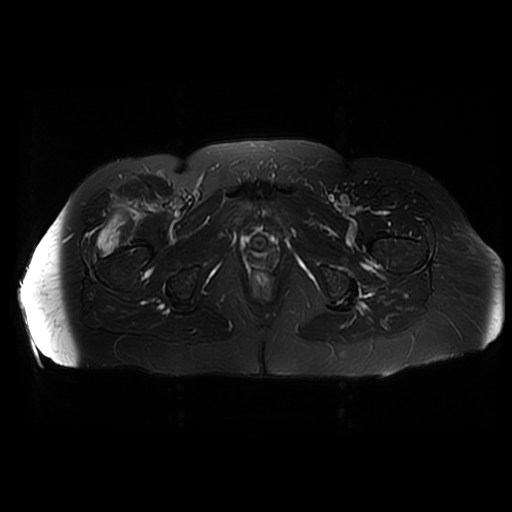
MRI of an extremity soft-tissue mass, one axial slice. Position 34 of 42 along the scan axis. T2-weighted fat-saturated. 6 mm slice thickness. 512 × 512 image matrix. Female patient. Case-level facts recorded for this patient, not image findings: histological type: pleiomorphic undifferentiated sarcoma; grade: high; site of the primary tumour: right quadricep.
Annotated regions visible in this slice (expert manual segmentation):
- gross tumour volume including surrounding oedema: bounding box [x1, y1, x2, y2] px = [95, 215, 123, 258]